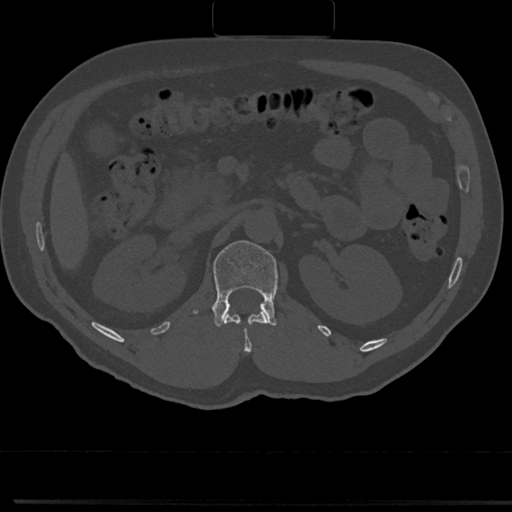
CT including the spine, one axial slice; slice 101 of 817 in the series (ordered by position); bone window (W 1800 / L 400 HU); 0.5 mm slice thickness; 512 × 512 image matrix. Patient: male, 61 years. Case-level facts recorded for this patient, not image findings: primary cancer: prostate.
Annotated regions visible in this slice (semi-automatically segmented with operator editing):
- L1 vertebra: bounding box [x1, y1, x2, y2] px = [191, 240, 278, 327]
- T12 vertebra: [234, 313, 267, 350]